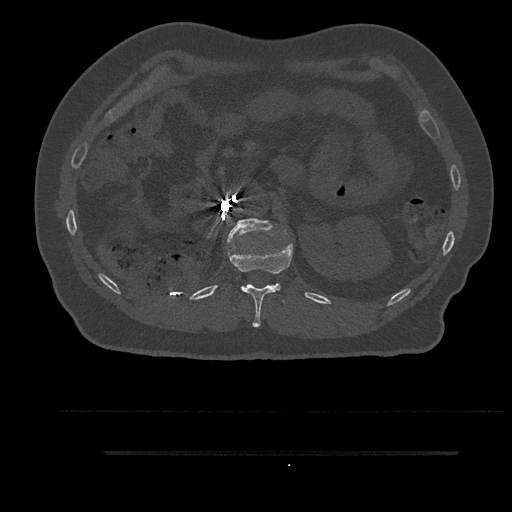
CT including the spine, one axial slice; position 223 of 797 along the scan axis; 120 kVp; bone window (W 1800 / L 400 HU); 0.5 mm slice thickness; 512 × 512 image matrix, field of view 432 × 432 mm. Male patient, age 63 years. From the clinical record (not read from this slice): primary cancer: renal.
Outlined on this slice (semi-automatically segmented with operator editing):
- L1 vertebra: box from (x=226, y=218) to (x=286, y=245) px
- T12 vertebra: (x=227, y=230)–(x=293, y=328)